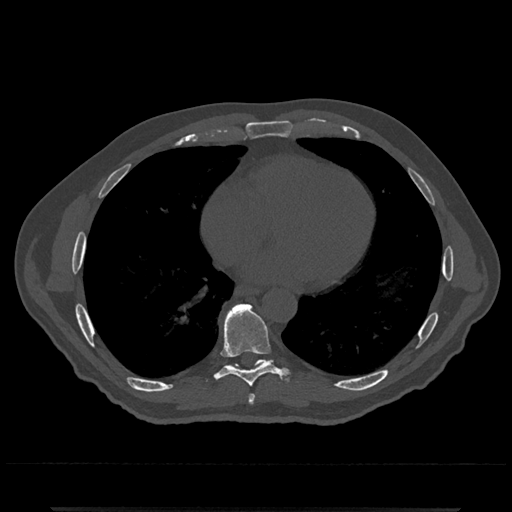
CT including the spine, one axial slice. Slice 663 of 797 in the series (ordered by position). Reconstruction kernel Br40s/3. Bone window (W 1800 / L 400 HU). 0.5 mm slice thickness. 512 × 512 image matrix, field of view 393 × 393 mm. Patient: male, 67 years. From the clinical record (not read from this slice): primary cancer: prostate.
Structures marked on this image (semi-automatic segmentation, software-assisted and operator-edited):
- T7 vertebra: bounding box <248,394,255,404> (left, top, right, bottom; pixels)
- T8 vertebra: <216,304,280,387>
- T9 vertebra: <226,365,236,368>